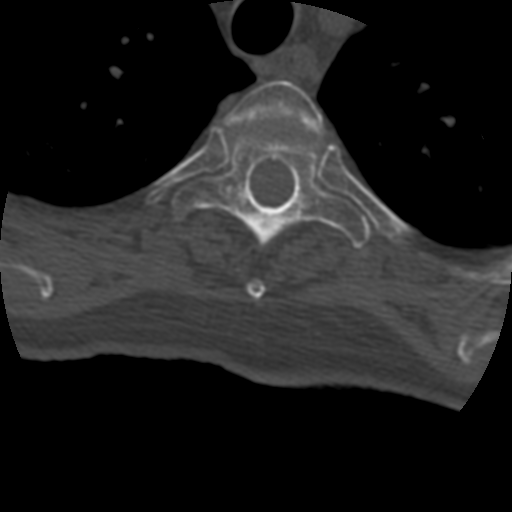
CT including the spine, one axial slice; 120 kVp; bone window (W 1800 / L 400 HU); 1.25 mm slice thickness; 512 × 512 image matrix, field of view 160 × 160 mm. Patient age 69 years. Case-level facts recorded for this patient, not image findings: primary cancer: prostate.
Structures marked on this image (semi-automatically segmented with operator editing):
- T3 vertebra: box from (x=227, y=80) to (x=323, y=299) px
- T4 vertebra: (x=172, y=132)–(x=370, y=249)